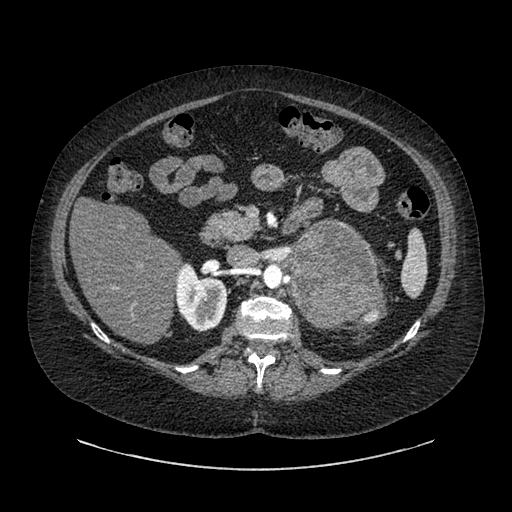
Contrast-enhanced abdominal CT, one axial slice; slice 537 of 769 in the series (ordered by position); reconstruction kernel SOFT; soft-tissue window (W 400 / L 40 HU); 0.62 mm slice thickness; 512 × 512 image matrix. Female patient, age 61 years. Case-level facts recorded for this patient, not image findings: diagnosis: adrenocortical carcinoma; tumour side: left adrenal; tumour size at pathology: 13 cm.
Structures marked on this image (semi-automatically segmented with operator editing):
- mass: box from (x=291, y=223) to (x=375, y=327) px